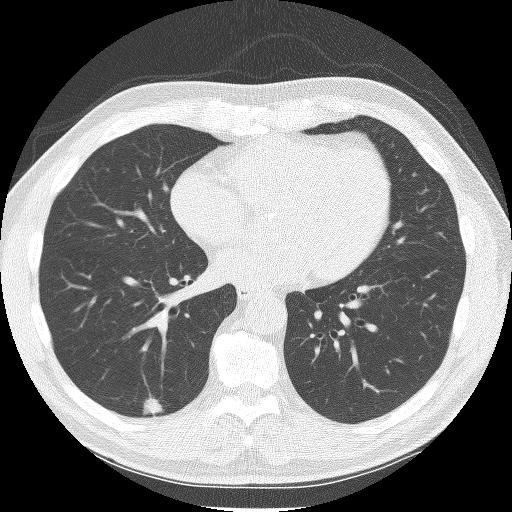
Chest CT (low-dose screening protocol), one axial image, baseline annual screen, lung window (W 1500 / L -600 HU), 2.5 mm slice thickness, lung (sharp) reconstruction kernel (BONE), 120 kVp, slice 87 of 150 in the series. Male participant, aged 61 years at enrolment. Current smoker at enrolment.
• Expert reader's lesion annotation, box from (x=127, y=385) to (x=172, y=424) px.
• Screening reader's record for this exam (one nodule recorded; not confirmed to be the boxed lesion): non-calcified nodule or mass ≥4 mm, right lower lobe, 12 × 11 mm, spiculated (stellate) margins, soft tissue attenuation.
• Official screen result: positive, change unspecified: nodule(s) >= 4 mm or enlarging nodule(s), mass(es), or other non-specific abnormalities suspicious for lung cancer.
• Participant outcome: lung cancer diagnosed 232 days after this screen — adenocarcinoma, NOS, right lower lobe, moderately differentiated (G2), stage IA (AJCC 6th edition), 9 mm at pathology.